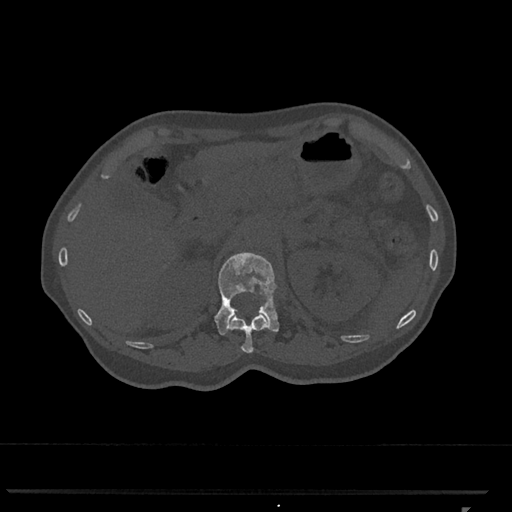
CT including the spine, one axial slice; slice 426 of 793 in the series (ordered by position); reconstruction kernel Br40s/3; bone window (W 1800 / L 400 HU); 0.5 mm slice thickness; 512 × 512 image matrix. Female patient, age 62 years. From the clinical record (not read from this slice): primary cancer: renal.
Structures marked on this image (semi-automatically segmented with operator editing):
- L1 vertebra: bounding box (x1, y1, x2, y2) in pixels: (214, 252, 279, 335)
- T12 vertebra: (229, 312, 267, 353)